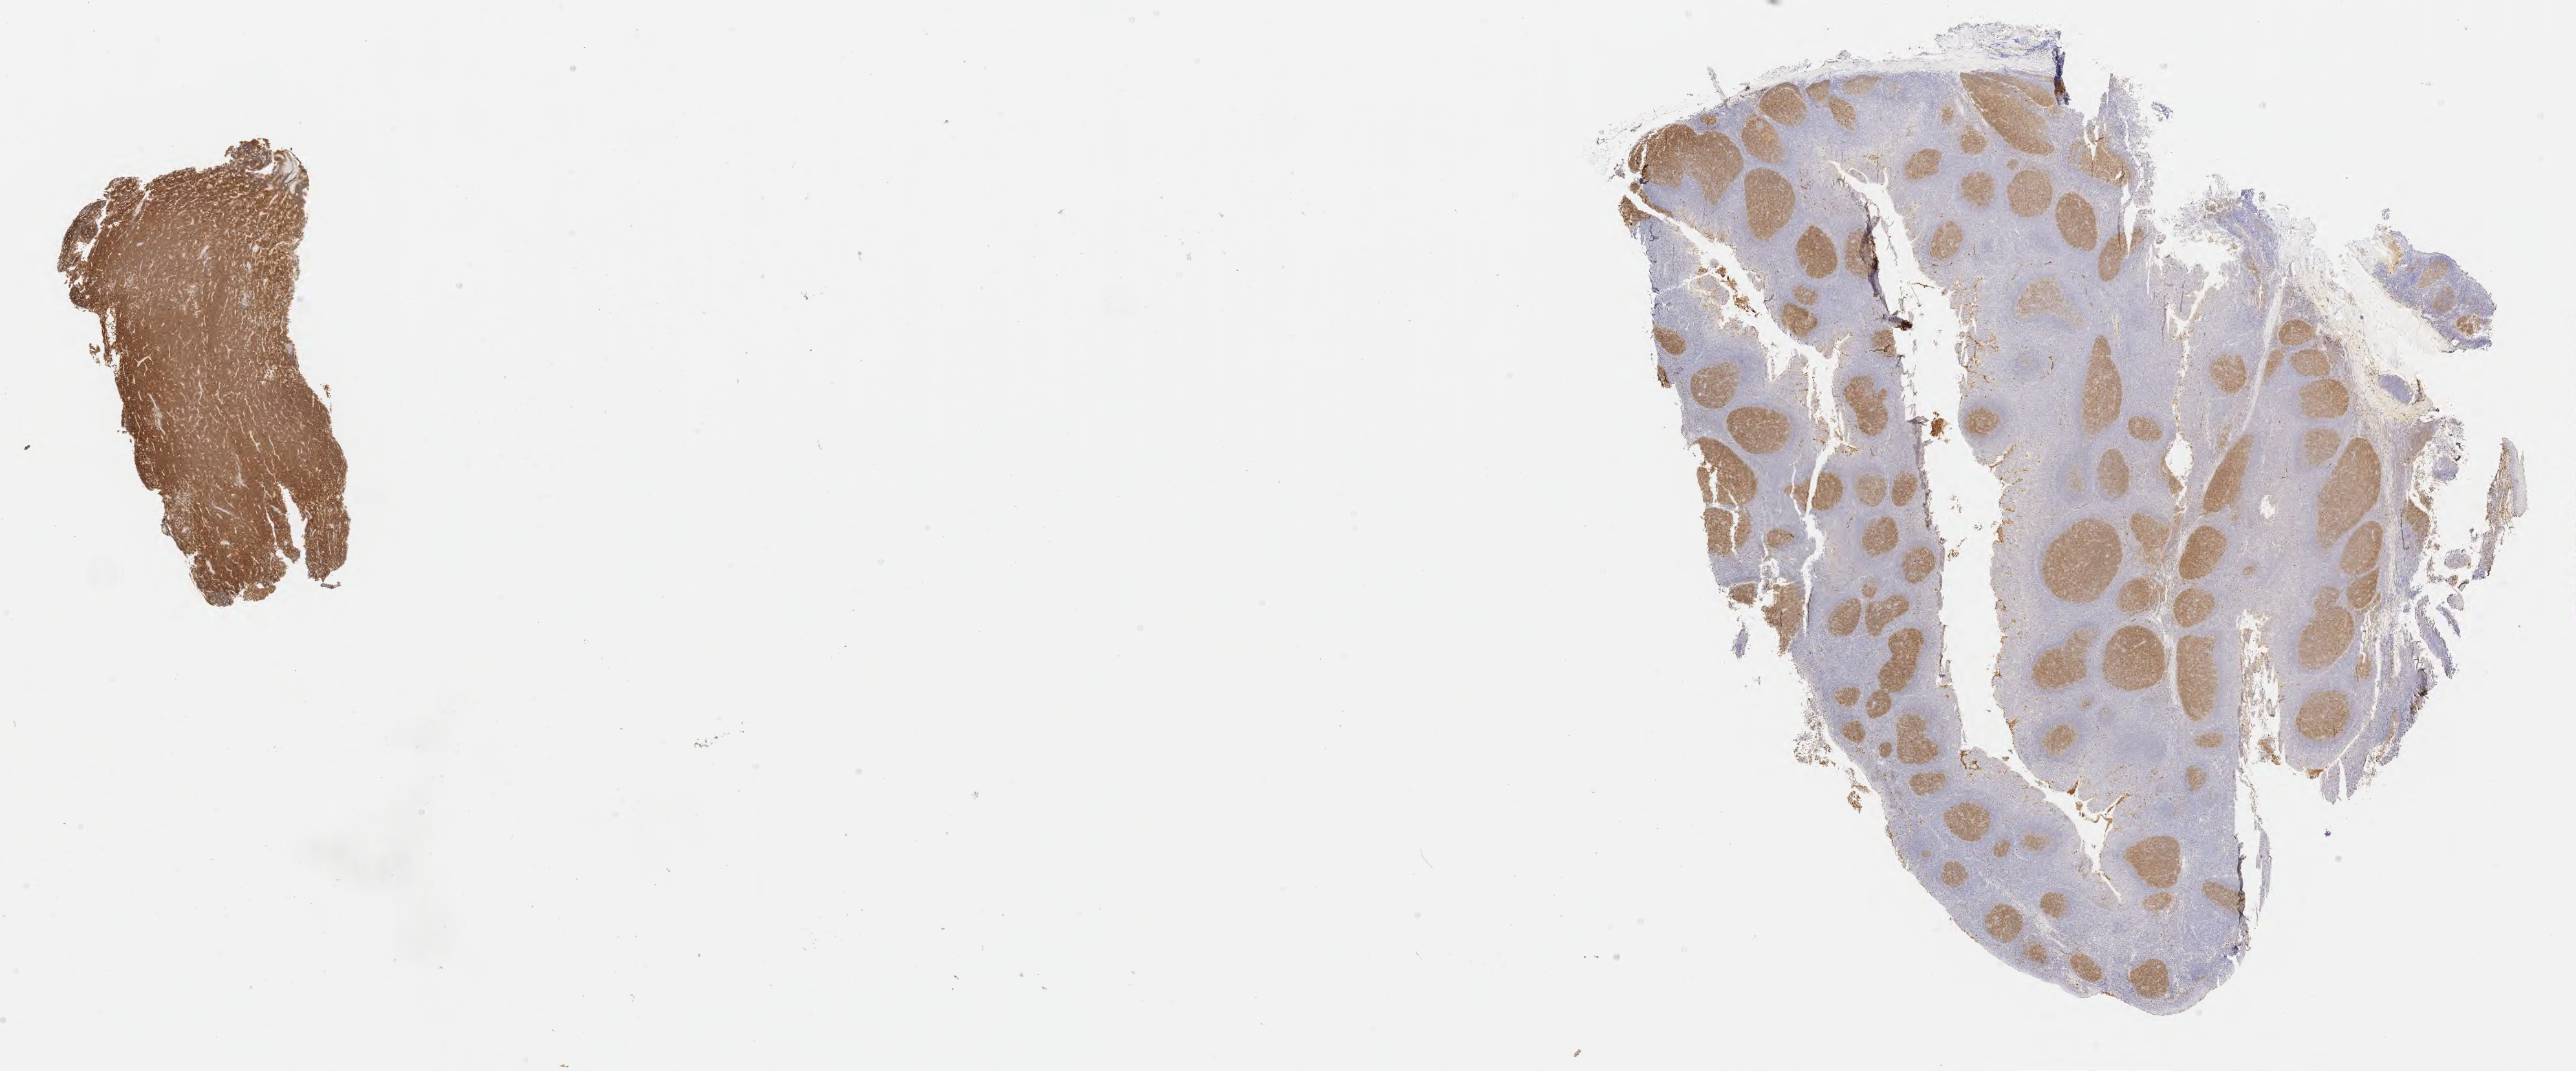
Immunohistochemistry (IHC) whole-slide image stained for CD10, low-resolution overview of the scanned area, about 32.2 x 13.4 mm, specimen: tumor tissue, site: cranium. Male patient, 11 years old.
Diagnosis: Diffuse large B-cell lymphoma, NOS.